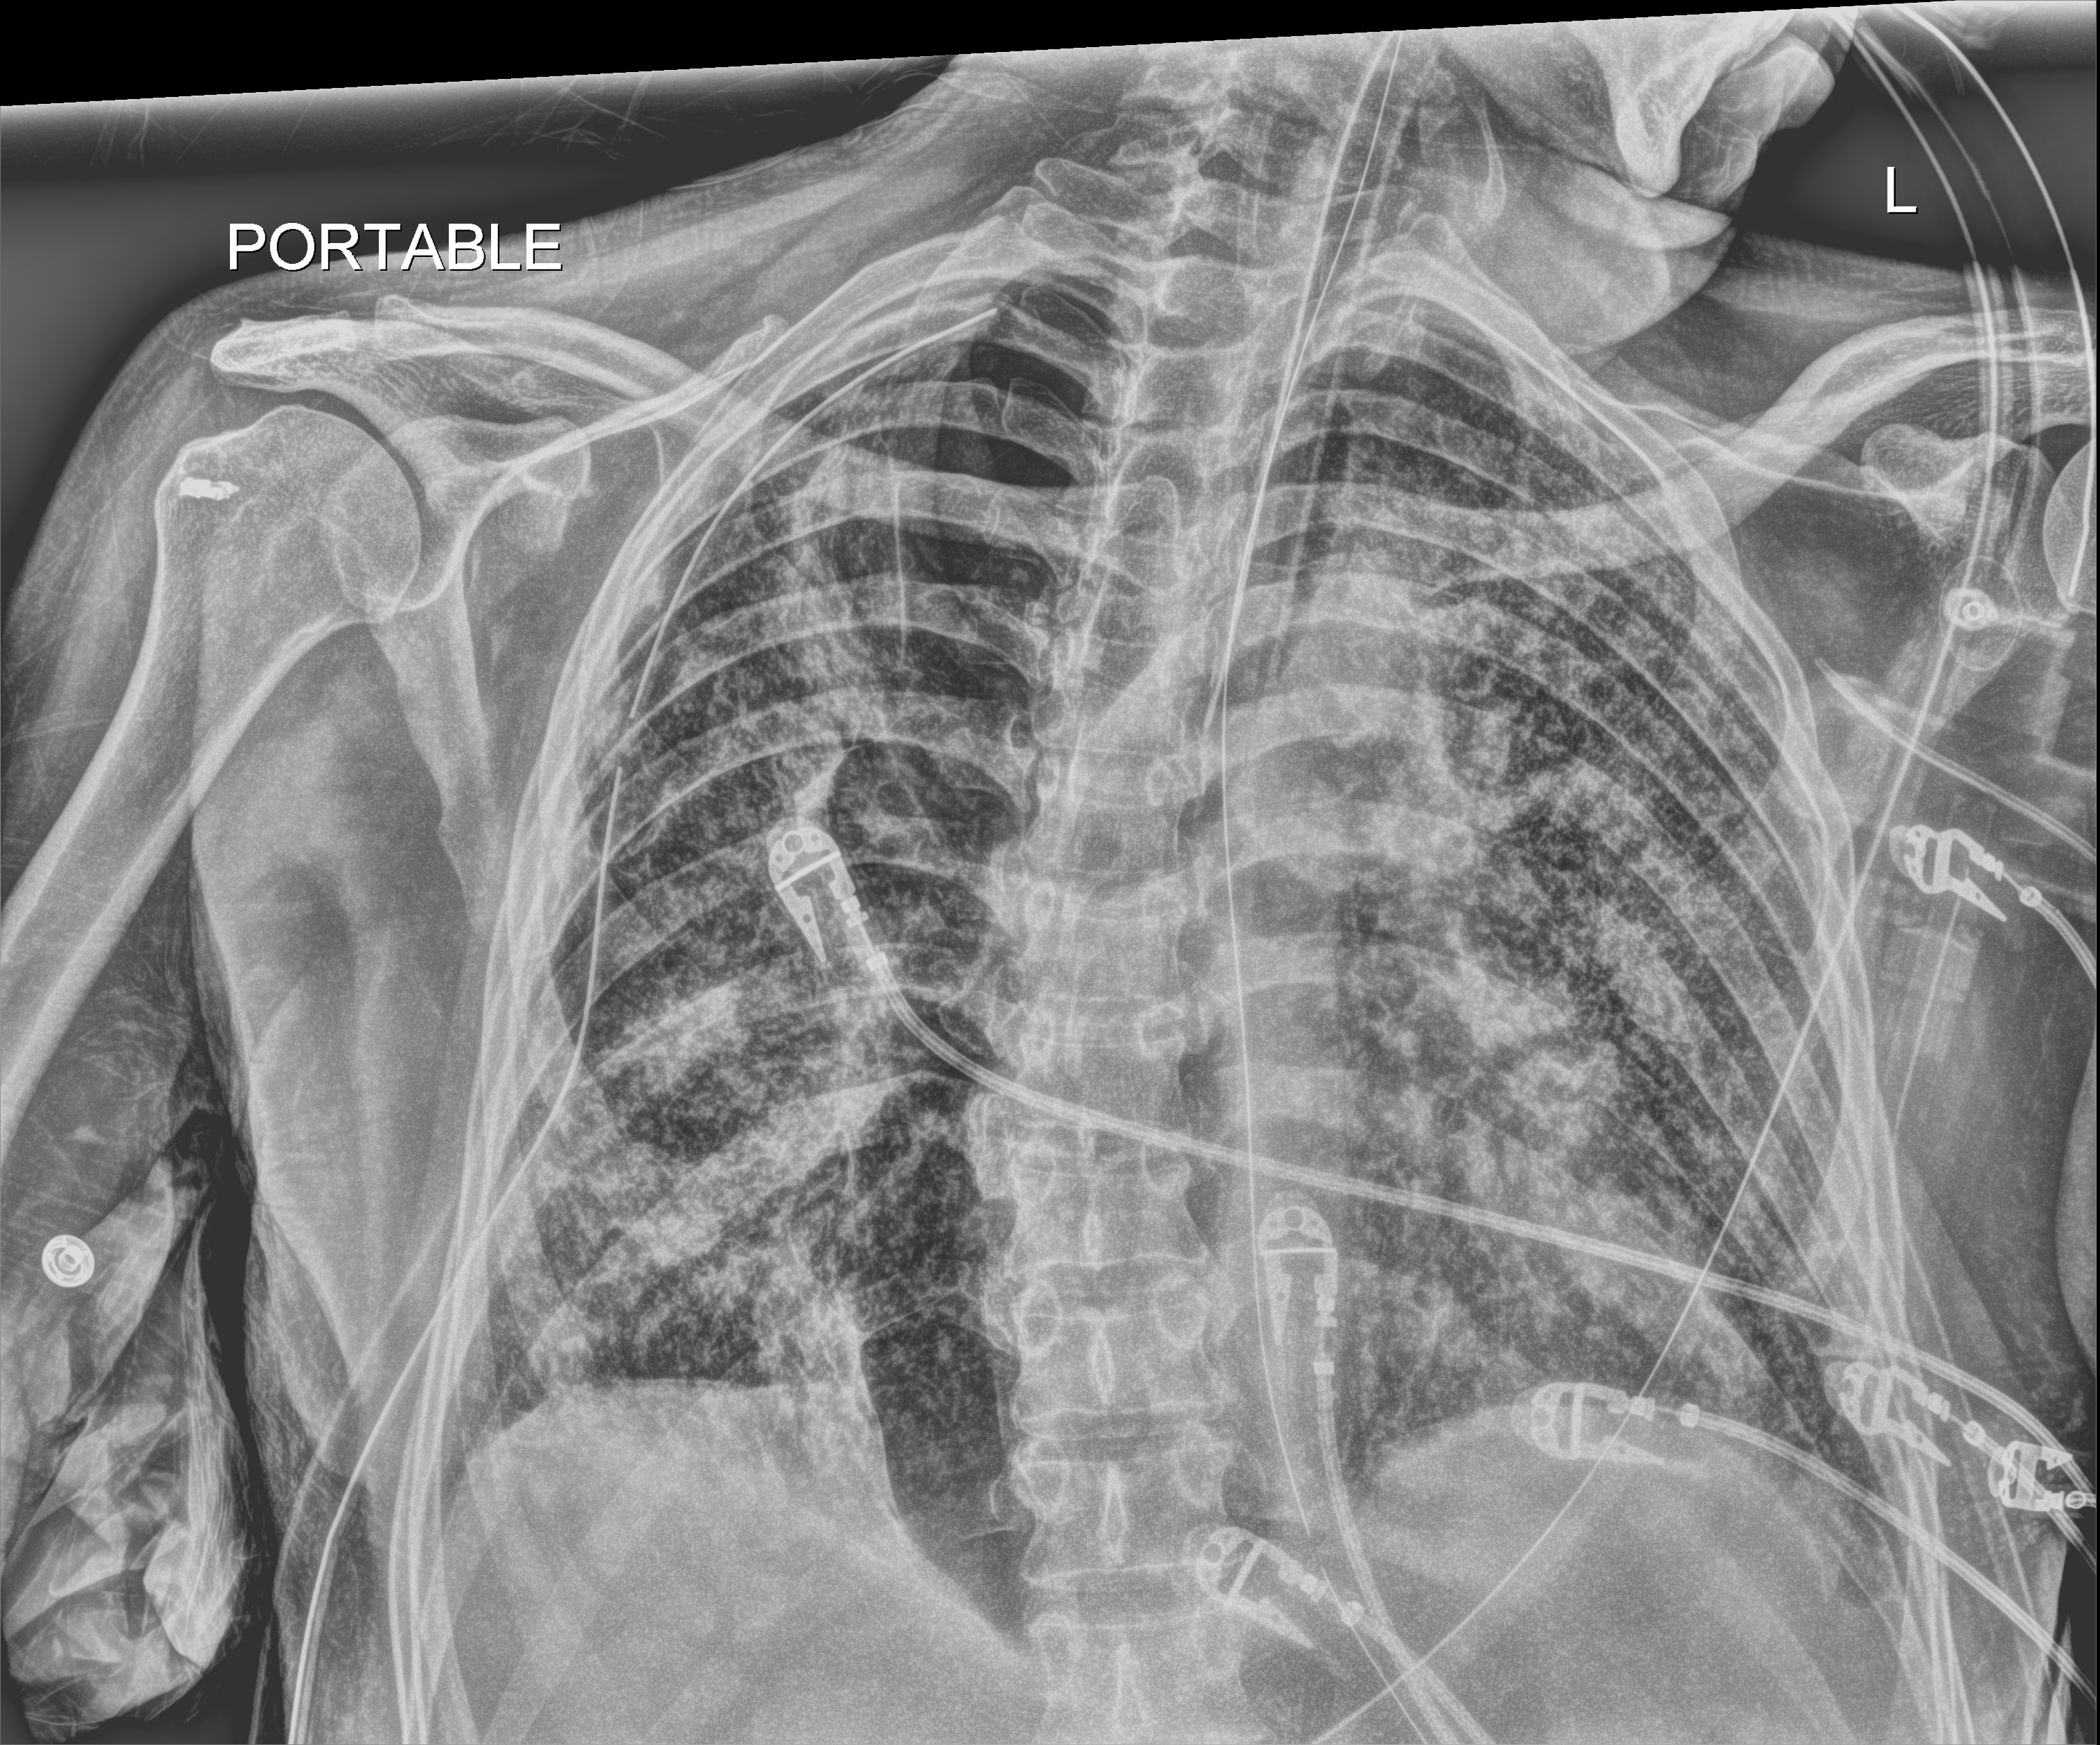
Chest X-ray (portable); anteroposterior (AP) projection. Patient hospitalised with COVID-19; male, aged 60–74 years.
Admission-level facts for this patient (not findings on this image; timing relative to this image not recorded):
- admitted to intensive care during this hospital stay: yes